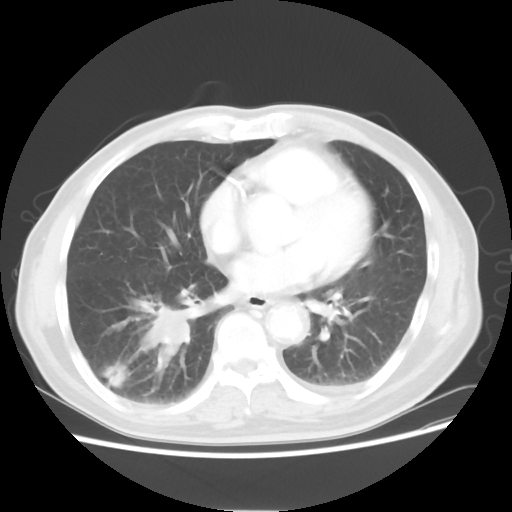
Chest CT, one axial slice; position 26 of 58 along the scan axis; lung window (W 1500 / L -600 HU); 512 × 512 image matrix, field of view 360 × 360 mm. Patient: male, 74 years. Case-level facts recorded for this patient, not image findings: clinical TNM (as recorded): T1c N1 M1.
Structures marked on this image (rectangle marked by the reading radiologist):
- lung tumour (recorded histology: adenocarcinoma): bounding box [x1, y1, x2, y2] px = [129, 290, 198, 369]